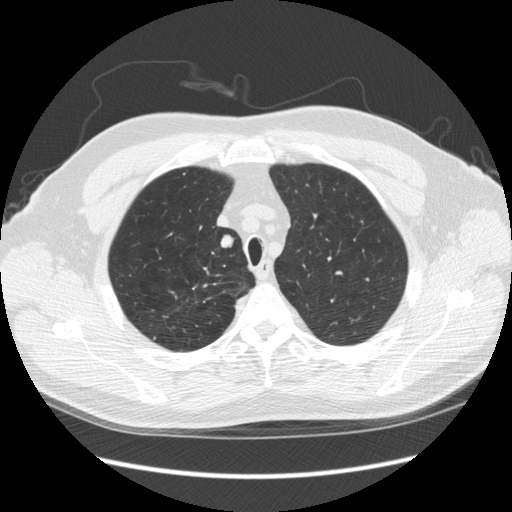
Chest CT (low-dose screening protocol), one axial image, third annual screen, lung window (W 1500 / L -600 HU), 2.5 mm slice thickness, standard (soft-tissue) reconstruction kernel (STANDARD), slice 41 of 248 in the series. Male, age 64 years at enrolment. Former smoker at enrolment.
Expert reader's lesion annotation, bounding box <198,230,241,262> (left, top, right, bottom; pixels). The screening reader recorded 4 non-calcified nodules or masses ≥4 mm on this exam (right upper lobe, right upper lobe, right upper lobe, right upper lobe); which of them this box marks is not recorded. Official screen result: positive, other. Lung cancer was diagnosed 15 days after this screen: adenocarcinoma, NOS, right upper lobe, moderately differentiated (G2), stage IA (AJCC 6th edition), 14 mm at pathology.